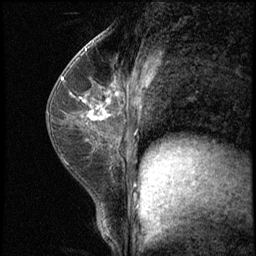
Breast MRI (dynamic contrast-enhanced), one sagittal slice. 3 images stored at this slice position (order not interpretable as contrast timing). 1.5 T. TE 4.2 ms, TR 8.7 ms. 2.5 mm slice thickness. 256 × 256 image matrix, field of view 180 × 180 mm. Female patient, age 35 years. From the clinical record (not read from this slice): setting: breast cancer imaged before/during neoadjuvant chemotherapy; receptor status: HER2-positive.
Annotated regions visible in this slice (semi-automatic segmentation, software-assisted and operator-edited):
- analysis volume of interest (the breast-tissue region the enhancement analysis was run in; not a lesion): box from (x=71, y=78) to (x=120, y=139) px
- tumour enhancement mask (voxels above the 140 % enhancement threshold inside the analysis volume of interest): (x=76, y=97)–(x=110, y=120)